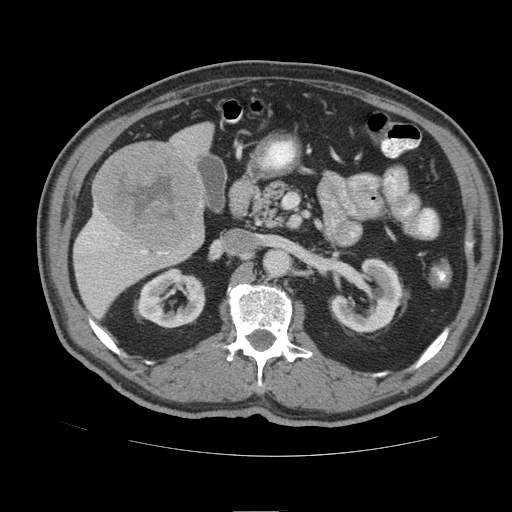
Contrast-enhanced abdominal CT (liver protocol), one axial slice. Slice 40 of 105 in the series (ordered by position). 140 kVp. Soft-tissue window (W 400 / L 40 HU). 512 × 512 image matrix, field of view 380 × 380 mm. From the clinical record (not read from this slice): diagnosis: hepatocellular carcinoma (patient treated with transarterial chemoembolisation; whether this scan precedes or follows treatment is not stated here); TNM stage (as recorded): Stage-IIIB; Child-Pugh class: A.
Structures marked on this image (semi-automatic segmentation, software-assisted and operator-edited):
- liver parenchyma outside the tumour (the mass and vessels are separate outlines, so this box may not span the whole liver): box from (x=74, y=122) to (x=214, y=318) px
- mass: (x=92, y=142)–(x=205, y=252)
- liver vessels: (x=83, y=209)–(x=163, y=255)